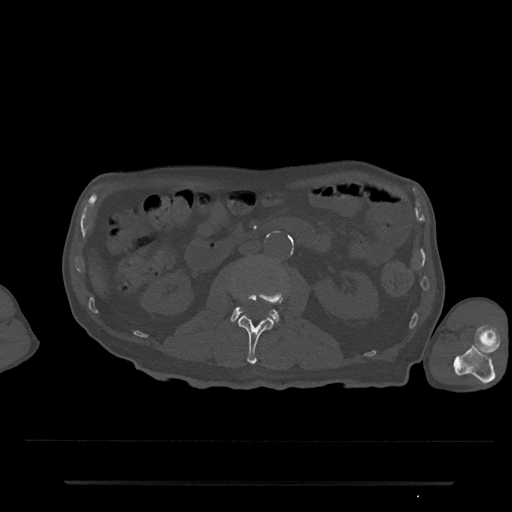
CT including the spine, one axial slice. Slice 34 of 797 in the series (ordered by position). Bone window (W 1800 / L 400 HU). 0.5 mm slice thickness. 512 × 512 image matrix, field of view 427 × 427 mm. Male patient, age 74 years. From the clinical record (not read from this slice): primary cancer: prostate.
Structures marked on this image (semi-automatically segmented with operator editing):
- L2 vertebra: bounding box (x1, y1, x2, y2) in pixels: (238, 284, 284, 365)
- L3 vertebra: (230, 306, 279, 323)